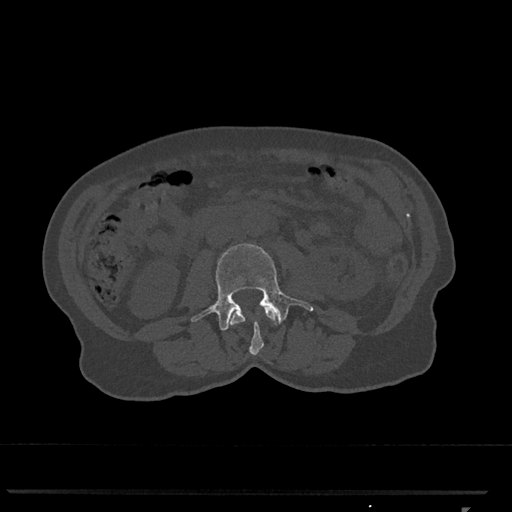
CT including the spine, one axial slice. Slice 291 of 793 in the series (ordered by position). Reconstruction kernel Br40s/3. Bone window (W 1800 / L 400 HU). 512 × 512 image matrix, field of view 380 × 380 mm. Patient: female, 62 years. Case-level facts recorded for this patient, not image findings: primary cancer: renal.
Annotated regions visible in this slice (semi-automatic segmentation, software-assisted and operator-edited):
- L2 vertebra: box from (x=229, y=306) to (x=278, y=355) px
- L3 vertebra: (x=191, y=243)–(x=313, y=330)